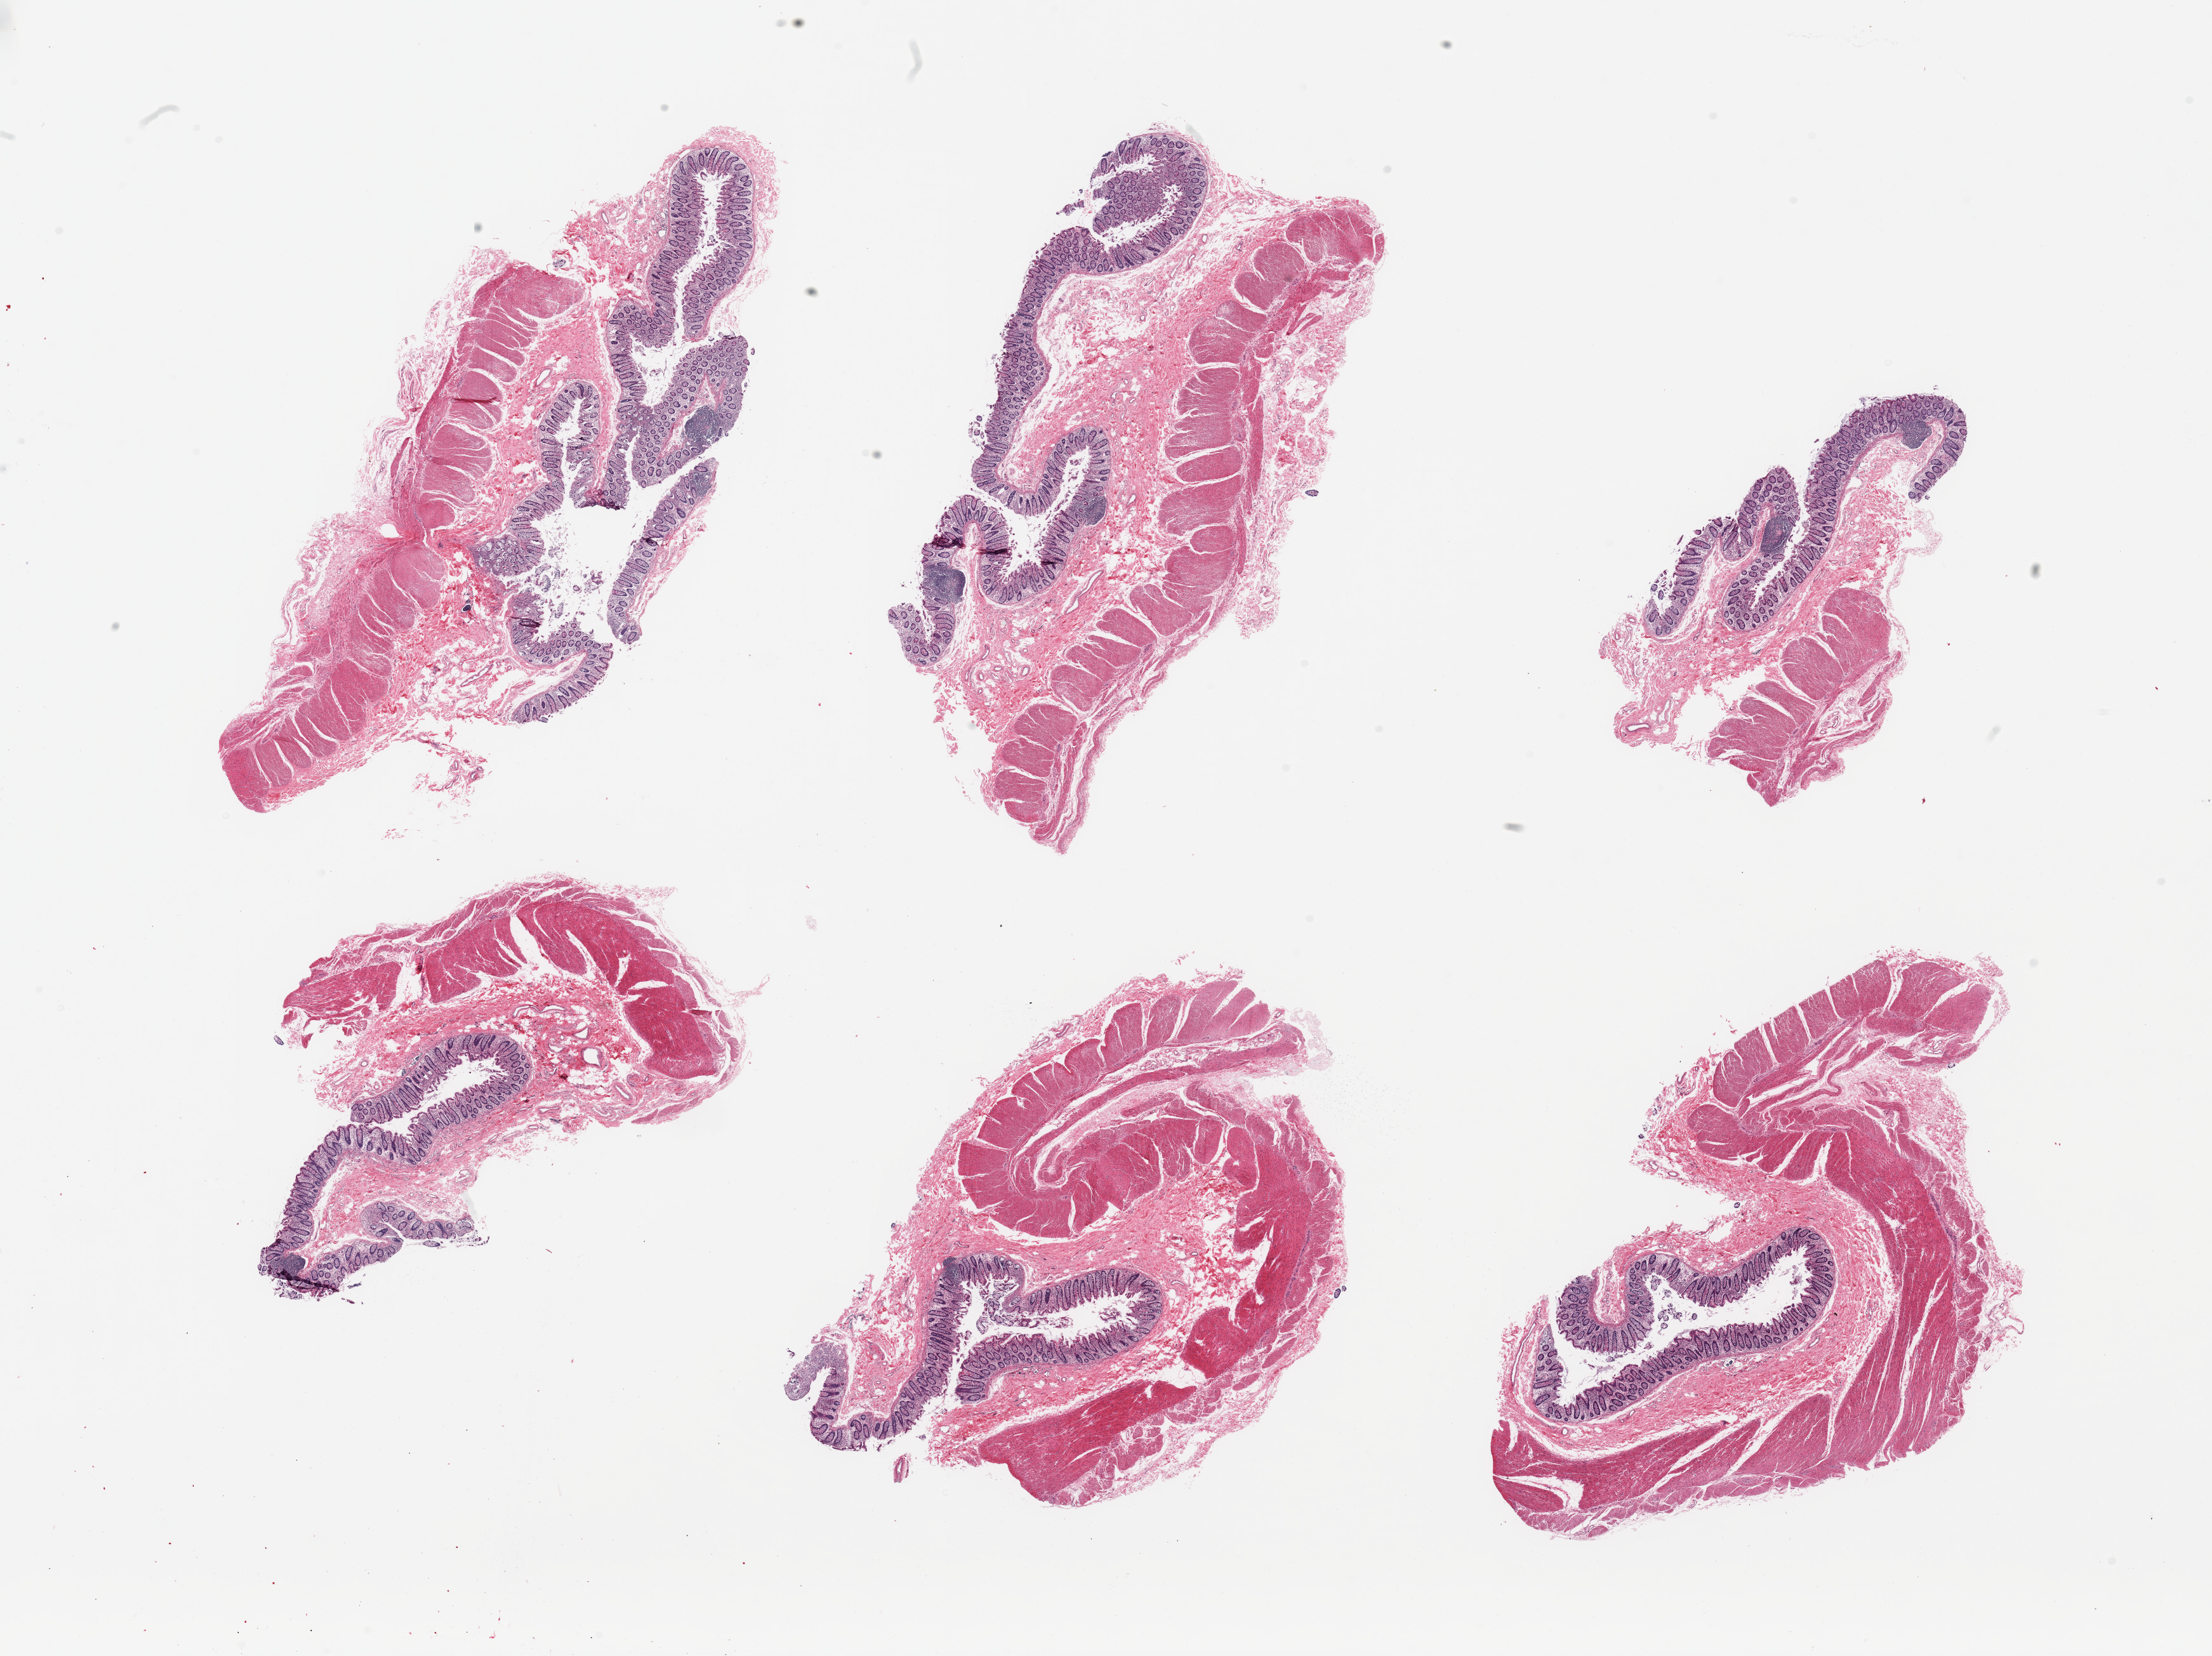
Digitized hematoxylin and eosin (H&E)-stained section, brightfield, shown as a low-resolution overview of the whole scanned area (about 27.6 x 20.6 mm), PAXgene-fixed, paraffin-embedded tissue, section of transverse colon (target tissue), donor tissue sample. Donor sex: female.
Pathologist's review note for this sample: 6 pieces; full thickness sections.